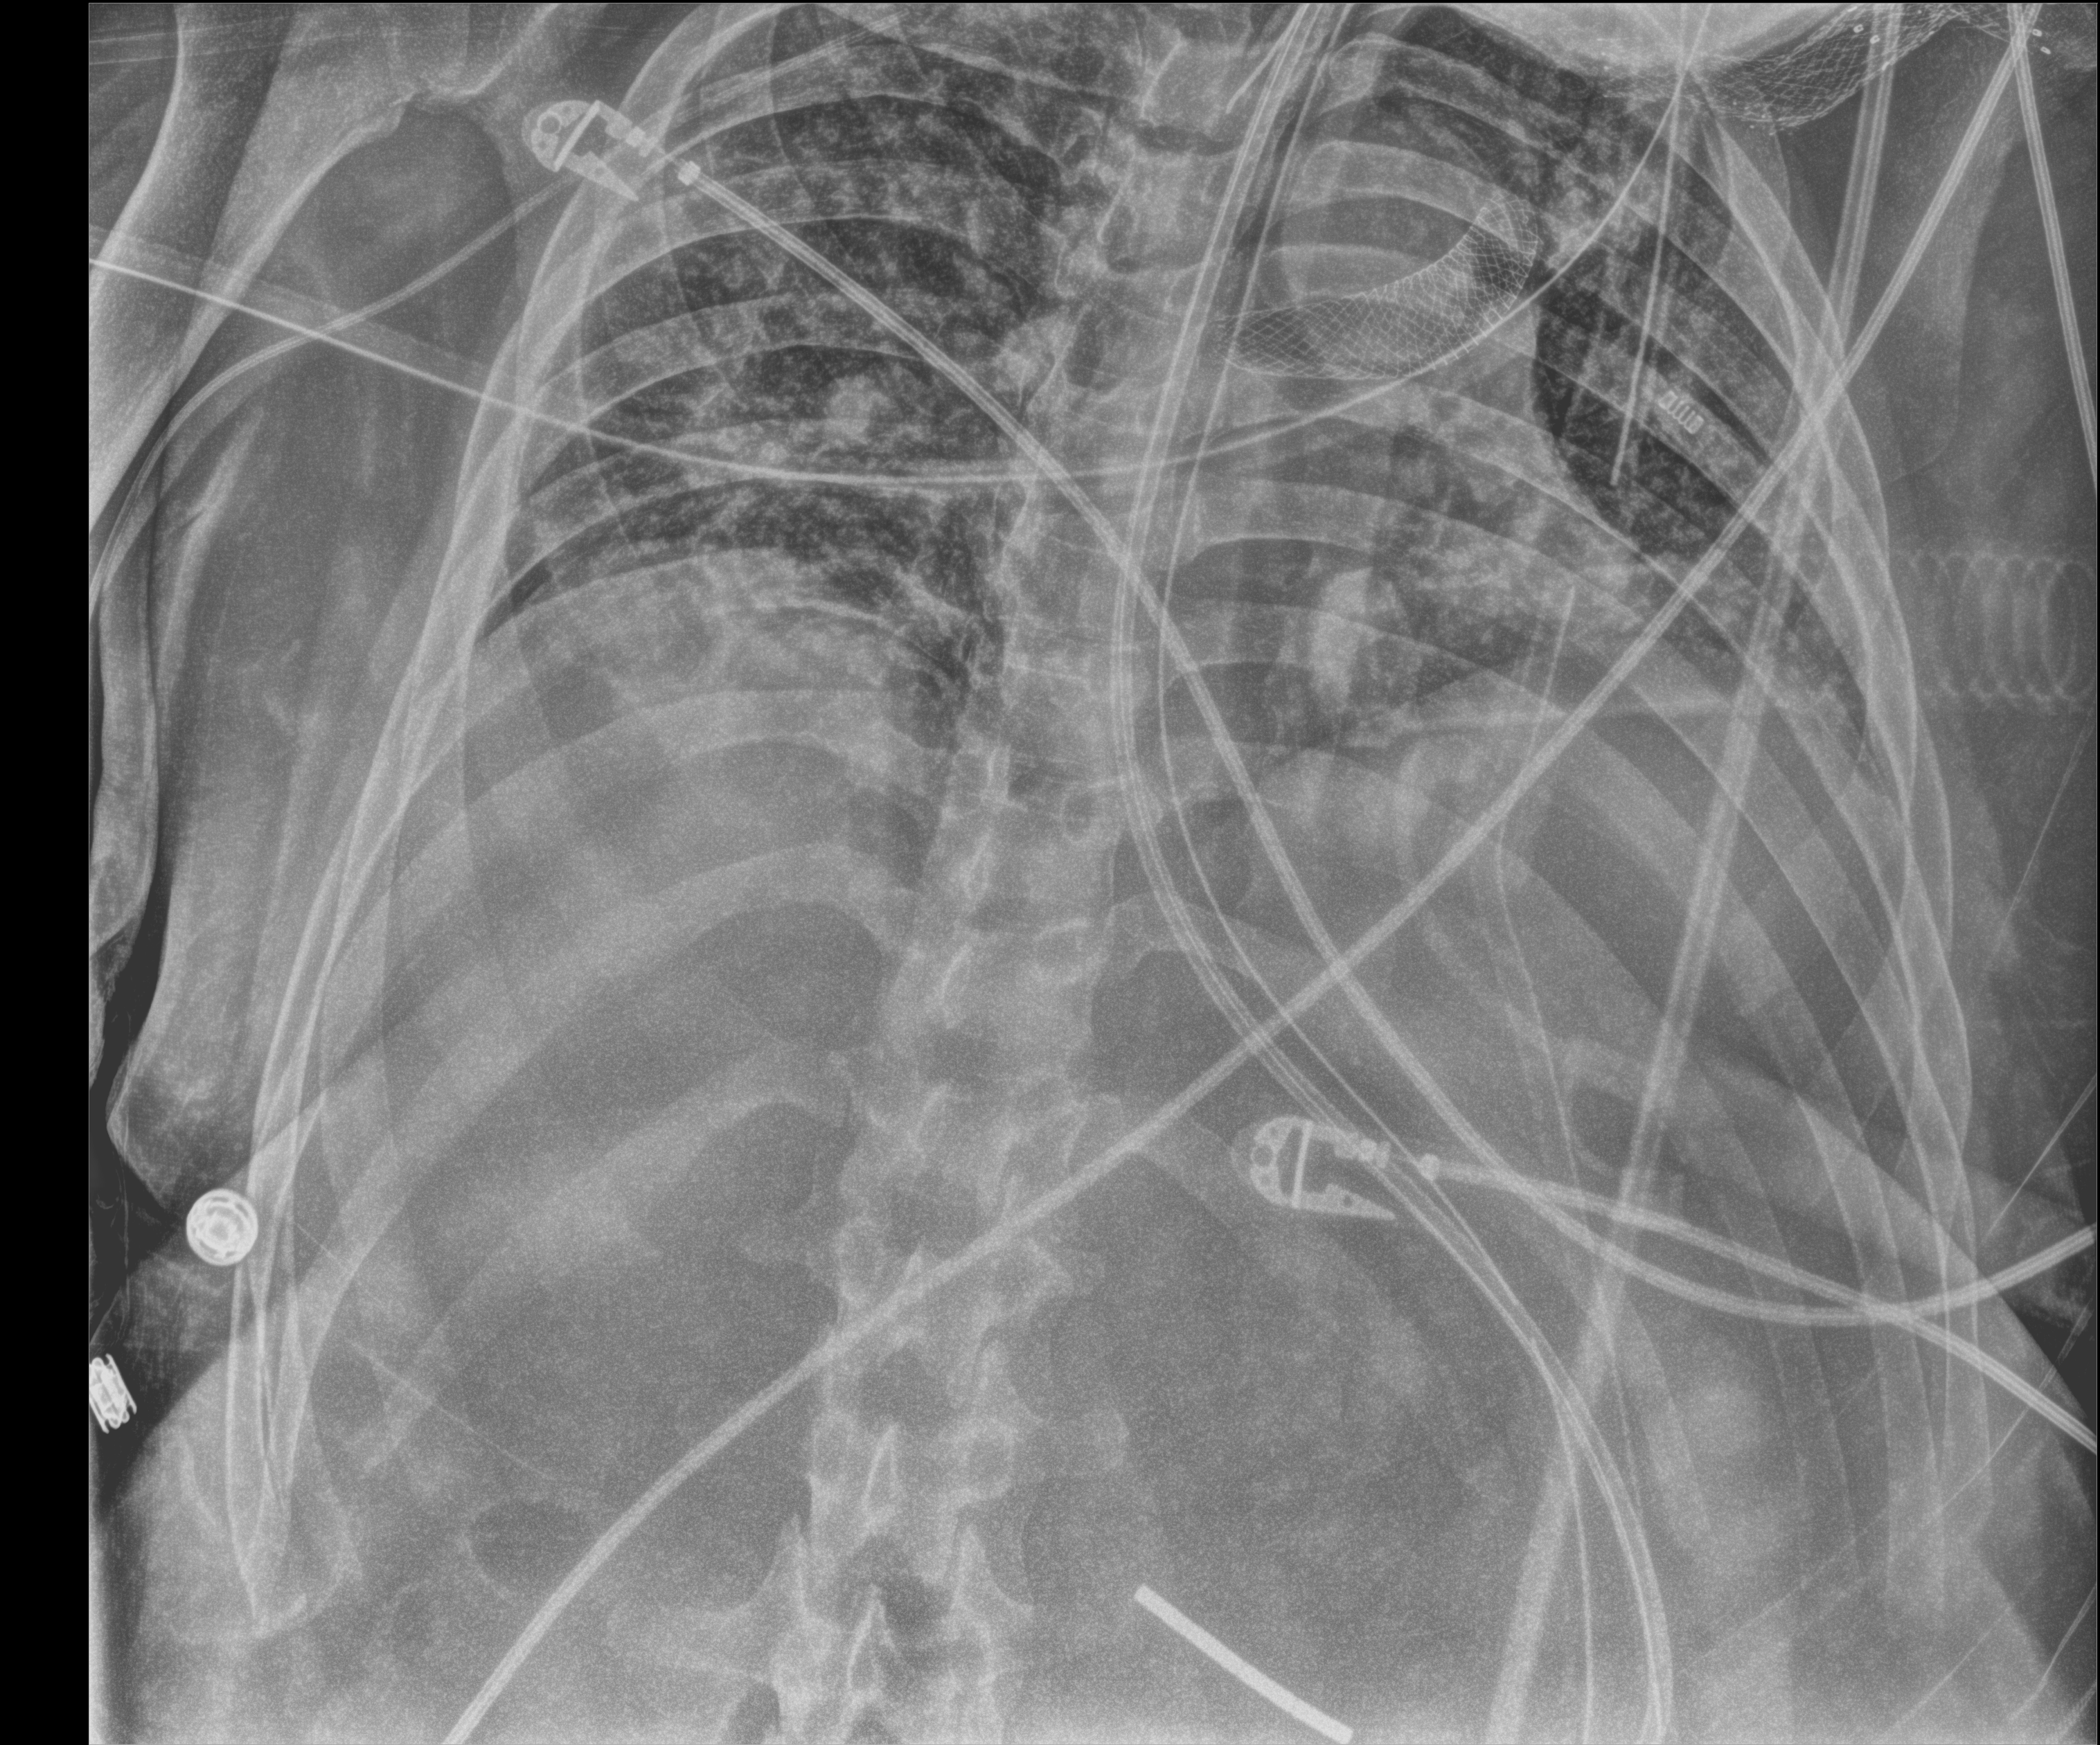
Chest X-ray (portable); anteroposterior (AP) projection. Male patient hospitalised with COVID-19, age 18–59 years.
From the hospital-stay record, not from the radiograph (when in the stay this image was taken is not recorded):
- COPD (admission record): no
- mechanically ventilated during this hospital stay: yes